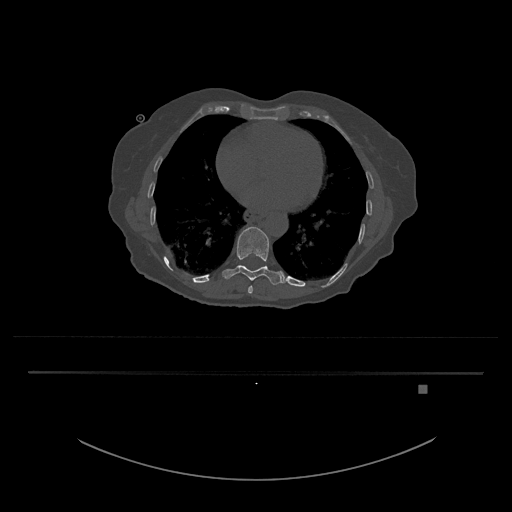
CT including the spine, one axial slice. Position 716 of 797 along the scan axis. Reconstruction kernel Br40s/3. 120 kVp. Bone window (W 1800 / L 400 HU). 0.5 mm slice thickness. 512 × 512 image matrix, field of view 500 × 500 mm. Female patient, age 57 years. Case-level facts recorded for this patient, not image findings: primary cancer: cervical.
Outlined on this slice (semi-automatically segmented with operator editing):
- T10 vertebra: bounding box <222,227,285,285> (left, top, right, bottom; pixels)
- T9 vertebra: <248,286,253,294>